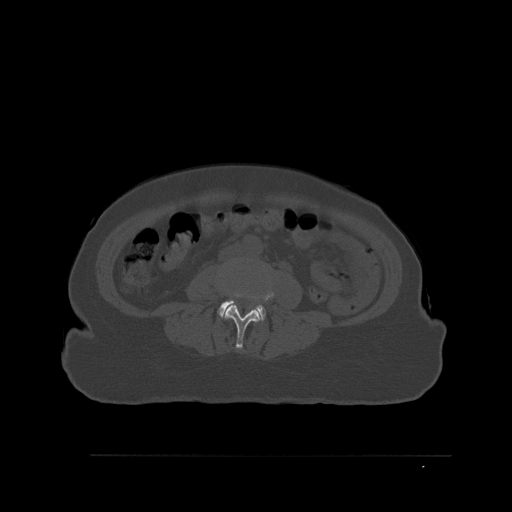
CT including the spine, one axial slice; slice 219 of 527 in the series (ordered by position); bone window (W 1800 / L 400 HU); 512 × 512 image matrix, field of view 470 × 470 mm. Female patient, age 73 years. From the clinical record (not read from this slice): primary cancer: breast; vertebrae with lytic lesions (as recorded): L2.
Outlined on this slice (semi-automatic segmentation, software-assisted and operator-edited):
- L3 vertebra: bounding box [x1, y1, x2, y2] px = [220, 280, 274, 349]
- L4 vertebra: [217, 300, 266, 321]